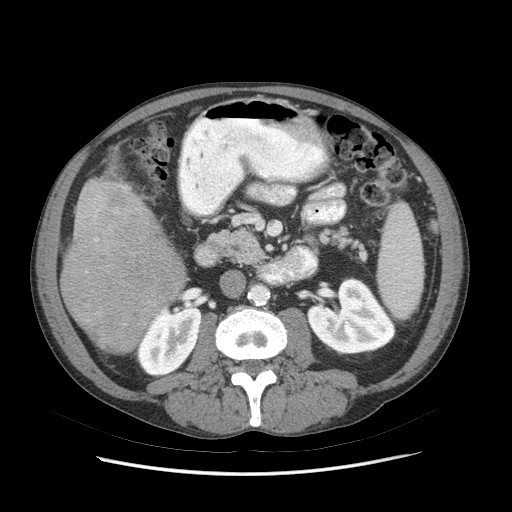
Contrast-enhanced abdominal CT (liver protocol), one axial slice; slice 24 of 89 in the series (ordered by position); soft-tissue window (W 400 / L 40 HU); 2.5 mm slice thickness; 512 × 512 image matrix, field of view 380 × 380 mm. From the clinical record (not read from this slice): diagnosis: hepatocellular carcinoma (patient treated with transarterial chemoembolisation; whether this scan precedes or follows treatment is not stated here); TNM stage (as recorded): Stage-IIIB.
Annotated regions visible in this slice (semi-automatic segmentation, software-assisted and operator-edited):
- liver parenchyma outside the tumour (the mass and vessels are separate outlines, so this box may not span the whole liver): bounding box [x1, y1, x2, y2] px = [60, 178, 186, 324]
- mass: [61, 214, 182, 354]